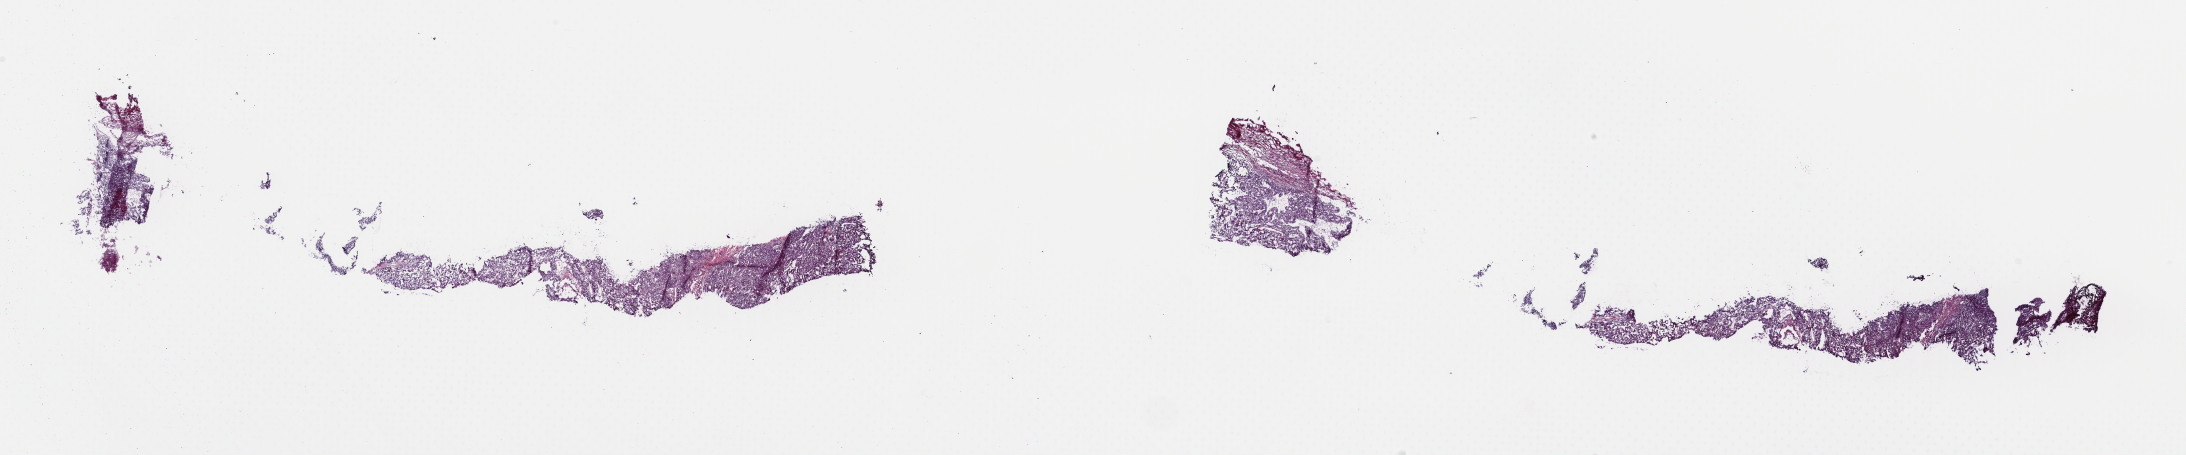
Whole-slide histology image, H&E-stained, a low-resolution overview of the entire scanned area, about 34.5 x 7.2 mm (slide scanned at 40x). Frozen section. Primary tumour sample from the kidney. Patient: female, age at initial diagnosis 35 years. Composition of this section per pathologist review: tumour cells 100%, tumour nuclei 80%, normal cells 0%, stromal cells 0%, necrosis 0%. Inflammatory infiltration, as recorded: lymphocyte infiltration 1%, monocyte infiltration 0%, neutrophil infiltration 0%.
Pathologic diagnosis: Papillary adenocarcinoma, NOS. Laterality: left. AJCC pathologic stage: III.